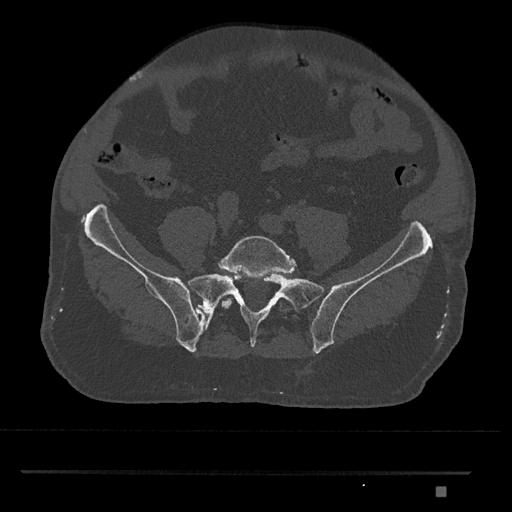
CT including the spine, one axial slice; position 524 of 1134 along the scan axis; reconstruction kernel Br40s/3; 120 kVp; bone window (W 1800 / L 400 HU); 0.5 mm slice thickness; 512 × 512 image matrix. Male patient, age 65 years. From the clinical record (not read from this slice): primary cancer: prostate.
Structures marked on this image (semi-automatically segmented with operator editing):
- L5 vertebra: bounding box <219,236,295,310> (left, top, right, bottom; pixels)